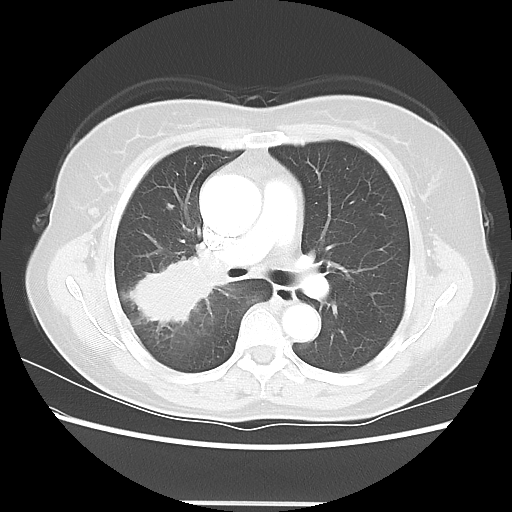
Chest CT, one axial slice; slice 36 of 56 in the series (ordered by position); reconstruction kernel LUNG; 120 kVp; lung window (W 1500 / L -600 HU); 512 × 512 image matrix. Female patient, age 55 years. From the clinical record (not read from this slice): clinical TNM (as recorded): T2 N1 M0; histopathological grade: G2-3.
Outlined on this slice (bounding box drawn by a radiologist):
- lung tumour (recorded histology: adenocarcinoma): bounding box (x1, y1, x2, y2) in pixels: (125, 257, 229, 332)